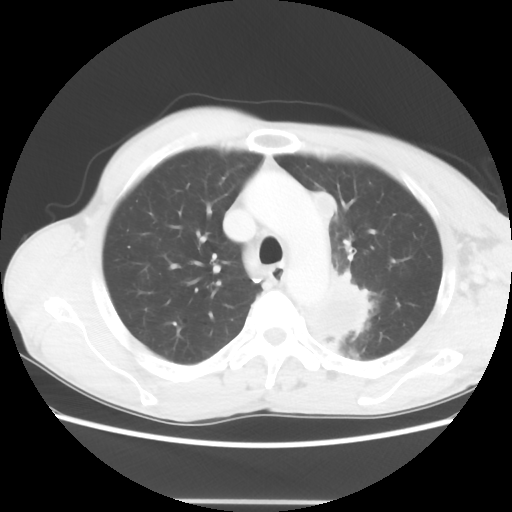
Chest CT, one axial slice; position 48 of 62 along the scan axis; reconstruction kernel STANDARD; lung window (W 1500 / L -600 HU); 512 × 512 image matrix. Patient: male, 61 years. Case-level facts recorded for this patient, not image findings: clinical TNM (as recorded): T3 N1 M1.
Structures marked on this image (rectangle marked by the reading radiologist):
- lung tumour (recorded histology: adenocarcinoma): bounding box <297,262,370,353> (left, top, right, bottom; pixels)
- lung tumour (recorded histology: adenocarcinoma): <315,193,339,221>